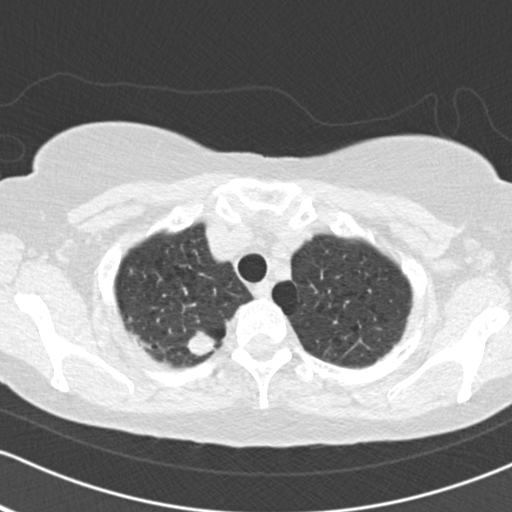
Low-dose screening chest CT, one axial slice; position 143 of 161 along the scan axis; 120 kVp; lung window (W 1500 / L -600 HU); 2 mm slice thickness; 512 × 512 image matrix, field of view 312 × 312 mm.
Structures marked on this image (expert manual segmentation):
- lesion 1 (tumor, upper lobe of right lung): bounding box <187,331,216,356> (left, top, right, bottom; pixels)